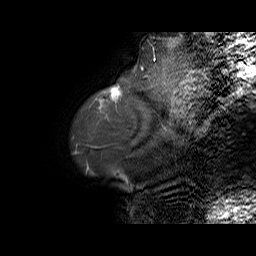
Breast MRI (dynamic contrast-enhanced), one sagittal slice; position 8 of 70 along the scan axis; dynamic contrast-enhanced series, time point 2 of 6 at this slice position (early post-contrast); 1.5 T; TE 5.5 ms, TR 32.9 ms; 4 mm slice thickness; 256 × 256 image matrix, field of view 240 × 240 mm. Female patient. Case-level facts recorded for this patient, not image findings: setting: breast cancer imaged before/during neoadjuvant chemotherapy; receptor status: HER2-positive.
Annotated regions visible in this slice (semi-automatically segmented with operator editing):
- analysis volume of interest (the breast-tissue region the enhancement analysis was run in; not a lesion): bounding box (x1, y1, x2, y2) in pixels: (99, 82, 141, 110)
- tumour enhancement mask (voxels above the 100 % enhancement threshold inside the analysis volume of interest): (101, 86, 119, 102)